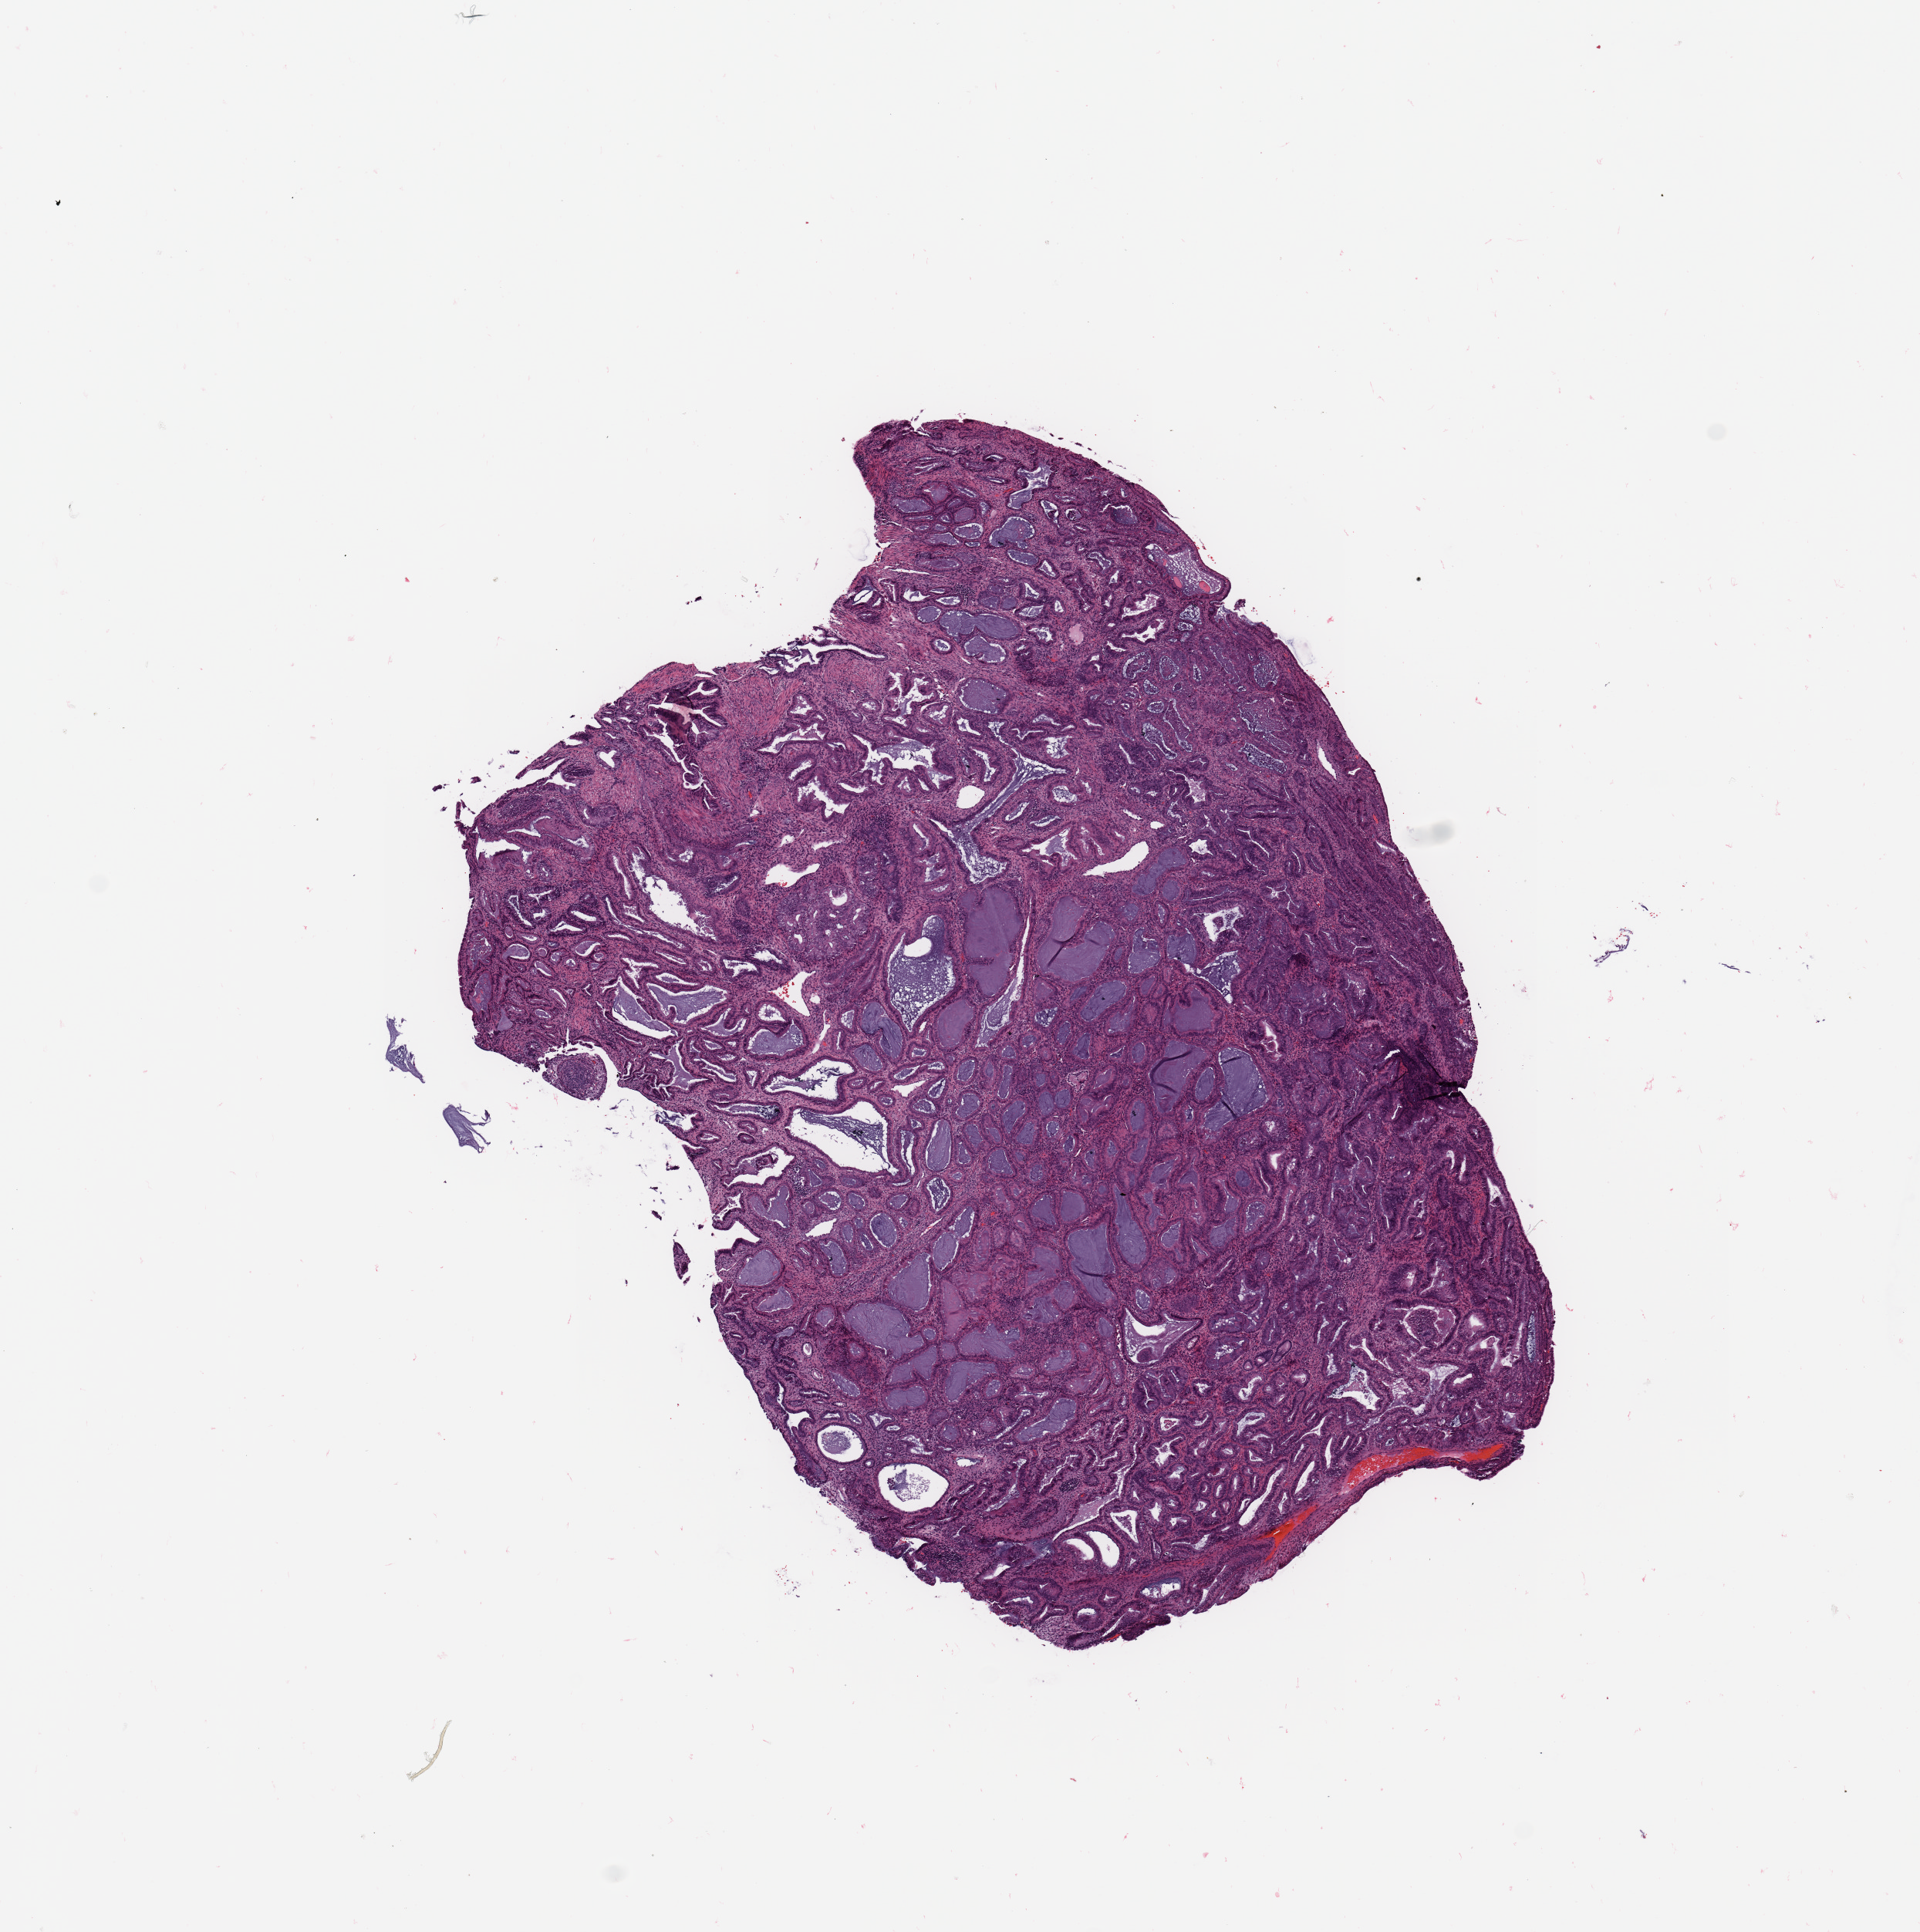
Whole-slide histology image, H&E-stained — a low-resolution overview of the entire scanned area, about 9.8 x 9.9 mm; tumour tissue sample, uterus. 56-year-old female patient. Histologic grade: G1 (well differentiated).
* histologic diagnosis: Endometrioid adenocarcinoma, NOS
* AJCC pathologic stage: II